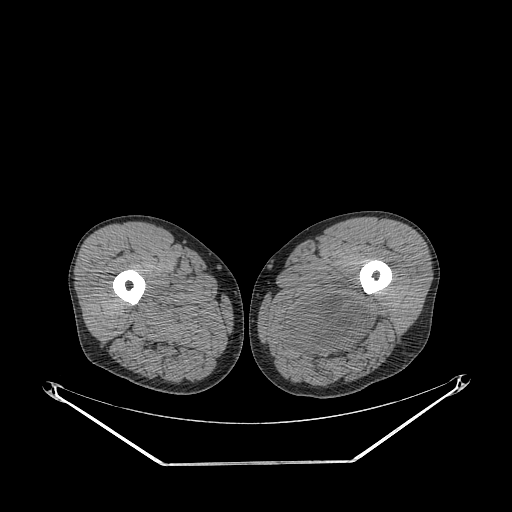
CT of an extremity soft-tissue mass (from a PET/CT study), one axial slice. Position 256 of 267 along the scan axis. Reconstruction kernel STANDARD. Soft-tissue window (W 400 / L 40 HU). 3.75 mm slice thickness. 512 × 512 image matrix. Male patient. From the clinical record (not read from this slice): histological type: undifferentiated pleomorphic liposarcoma; grade: high; site of the primary tumour: left thigh.
Annotated regions visible in this slice (expert contour drawn on MRI and transferred to this co-registered scan by the dataset authors):
- gross tumour volume including surrounding oedema: bounding box (x1, y1, x2, y2) in pixels: (281, 294, 368, 357)
- gross tumour volume (mass): (288, 295, 360, 353)